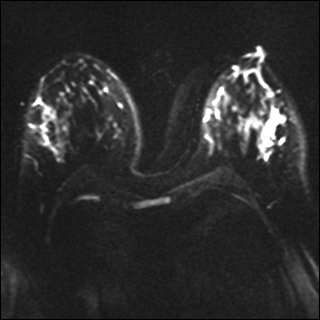
Breast MRI, one axial slice; position 17 of 41 along the scan axis; diffusion-weighted series; image 2 of 4 stored at this slice position (different b-values; order by instance number); 1.5 T; 4 mm slice thickness; 320 × 320 image matrix. Female patient.
Outlined on this slice (manually delineated by an expert):
- tumour on diffusion-weighted imaging: bounding box (x1, y1, x2, y2) in pixels: (264, 126, 273, 139)